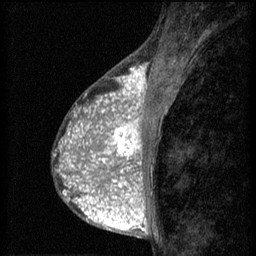
Breast MRI (dynamic contrast-enhanced), one sagittal slice; slice 27 of 60 in the series (ordered by position); 3 images stored at this slice position (order not interpretable as contrast timing); 1.5 T; TE 4.2 ms, TR 8.2 ms; 2 mm slice thickness; 256 × 256 image matrix, field of view 180 × 180 mm. Female patient, age 38 years.
Structures marked on this image (semi-automatic segmentation, software-assisted and operator-edited):
- analysis volume of interest (the breast-tissue region the enhancement analysis was run in; not a lesion): bounding box [x1, y1, x2, y2] px = [92, 112, 152, 171]
- tumour enhancement mask (voxels above the 70 % enhancement threshold inside the analysis volume of interest): [92, 112, 144, 171]